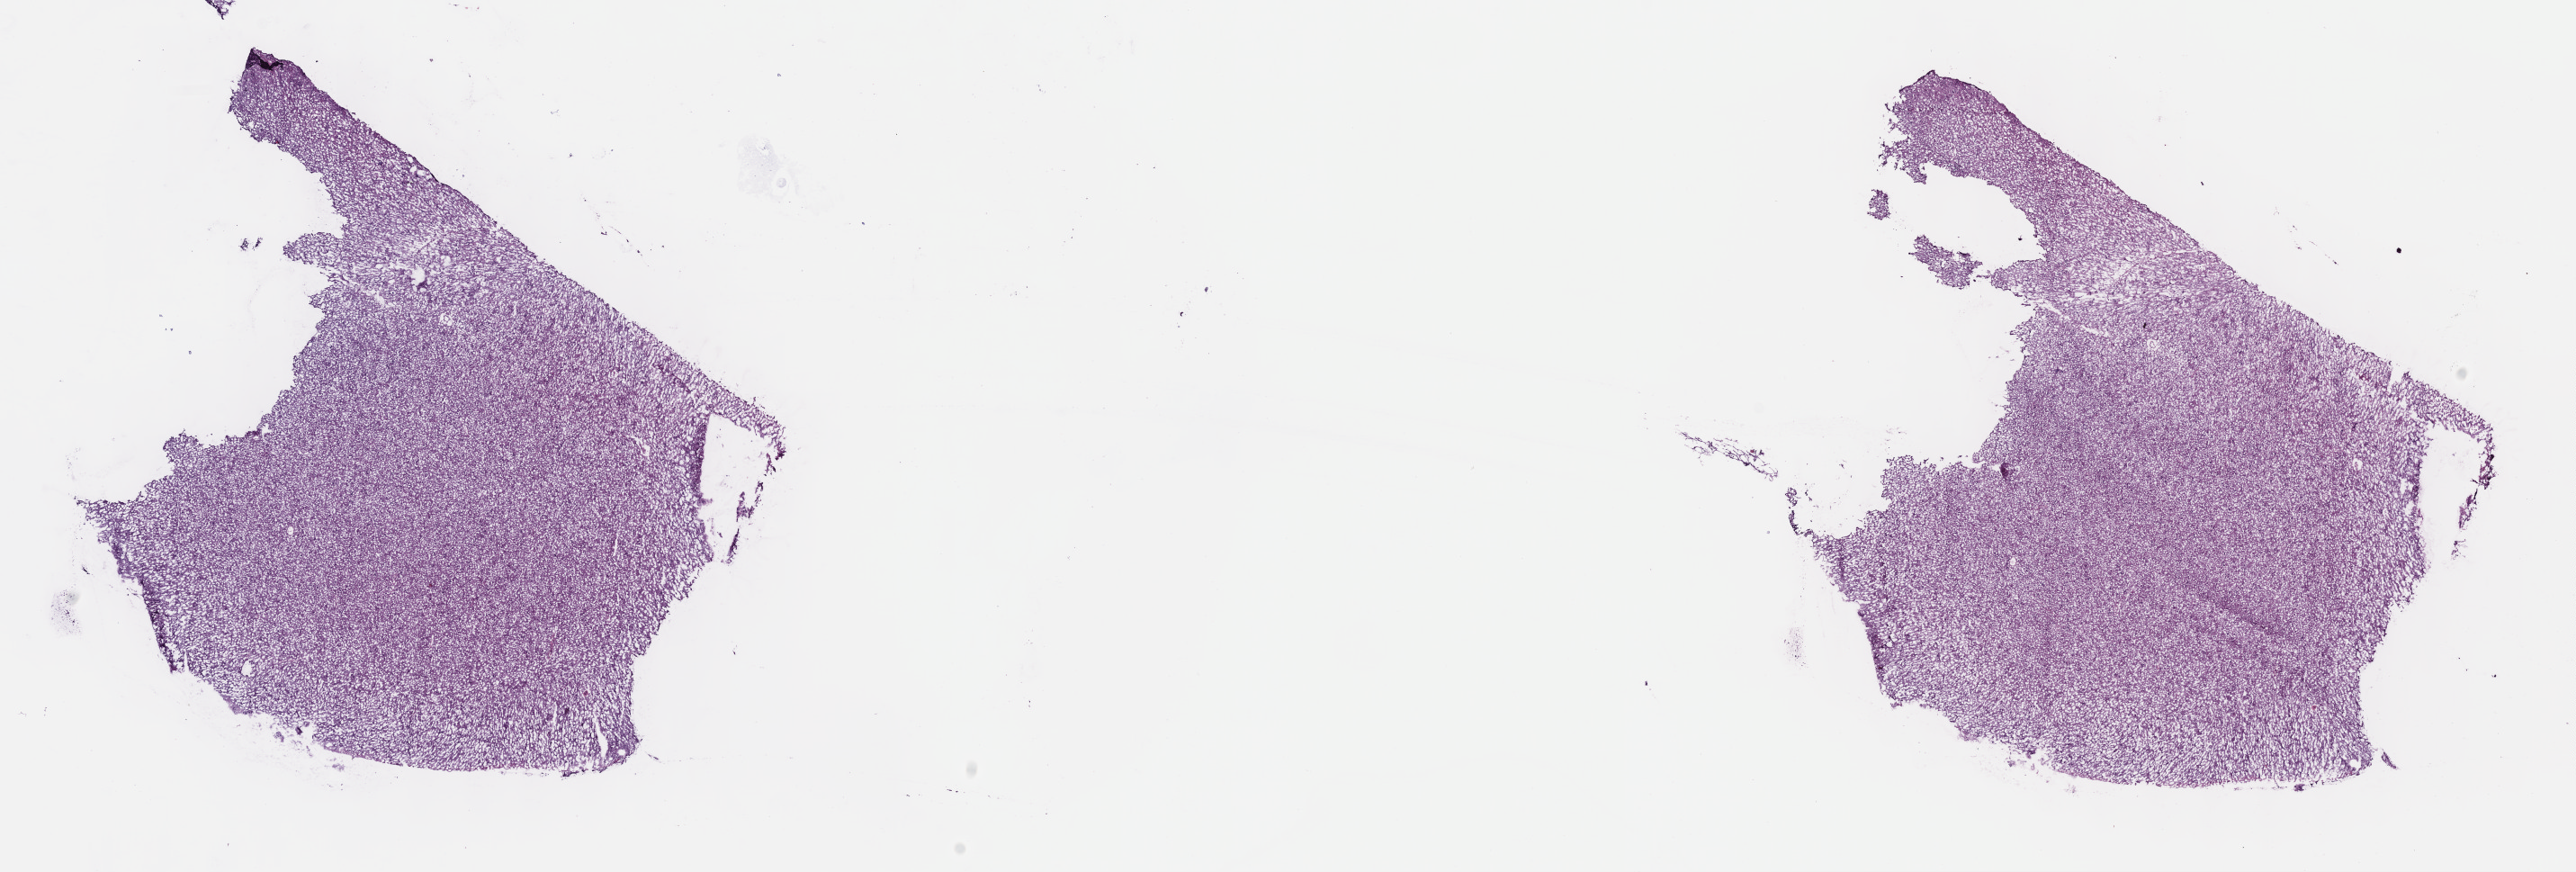
Whole-slide histology image, H&E — low-resolution overview of the scanned area, about 23.2 x 7.8 mm (from a 40x scan); frozen section from the top of the tissue portion; primary tumour sample from the brain. Patient: male, age at initial diagnosis 47 years. Histologic grade: G2 (moderately differentiated). Pathologist review of this section (percent, as recorded): tumour cells 45%, tumour nuclei 85%, normal cells 10%, stromal cells 45%, necrosis 0%. Inflammatory infiltration, as recorded: lymphocyte infiltration 0%, monocyte infiltration 0%, neutrophil infiltration 0%.
Histologic diagnosis: Oligodendroglioma, NOS (cerebrum).